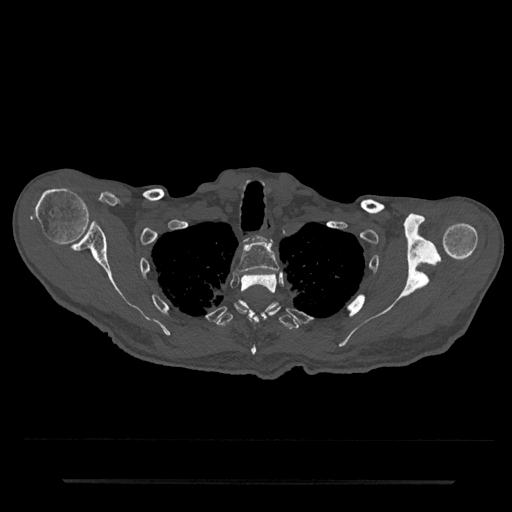
CT including the spine, one axial slice. Slice 656 of 797 in the series (ordered by position). Reconstruction kernel Br40s/3. 120 kVp. Bone window (W 1800 / L 400 HU). 0.5 mm slice thickness. 512 × 512 image matrix. Patient: male, 74 years. Case-level facts recorded for this patient, not image findings: primary cancer: prostate.
Outlined on this slice (semi-automatically segmented with operator editing):
- T1 vertebra: bounding box (x1, y1, x2, y2) in pixels: (257, 235, 272, 242)
- T2 vertebra: (236, 242, 279, 274)
- T3 vertebra: (235, 274, 280, 355)
- T4 vertebra: (216, 300, 300, 329)